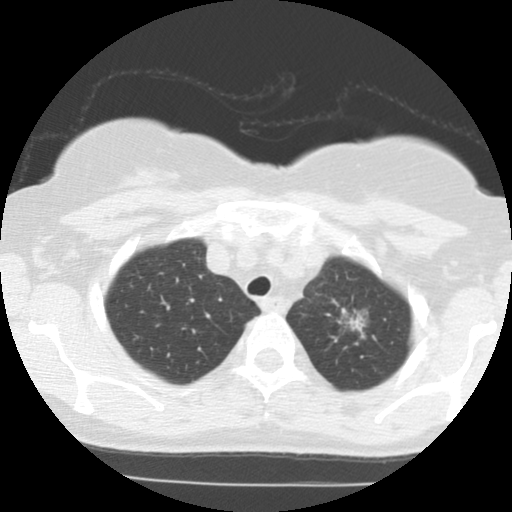
Chest CT (low-dose screening protocol), one axial image; baseline annual screen; lung window (W 1500 / L -600 HU); standard (soft-tissue) reconstruction kernel (STANDARD); slice 100 of 123 in the series. Female, age 61 years at enrolment.
Lesion marked by an expert reader, bounding box [x1, y1, x2, y2] px = [321, 299, 385, 351]. The screening reader recorded 2 non-calcified nodules or masses ≥4 mm on this exam (right lower lobe, left upper lobe); which of them this box marks is not recorded. Official screen result: positive, change unspecified: nodule(s) >= 4 mm or enlarging nodule(s), mass(es), or other non-specific abnormalities suspicious for lung cancer. Participant outcome: lung cancer diagnosed 79 days after this screen — adenocarcinoma, NOS, left upper lobe, stage IIIB (AJCC 6th edition), 15 mm at pathology.